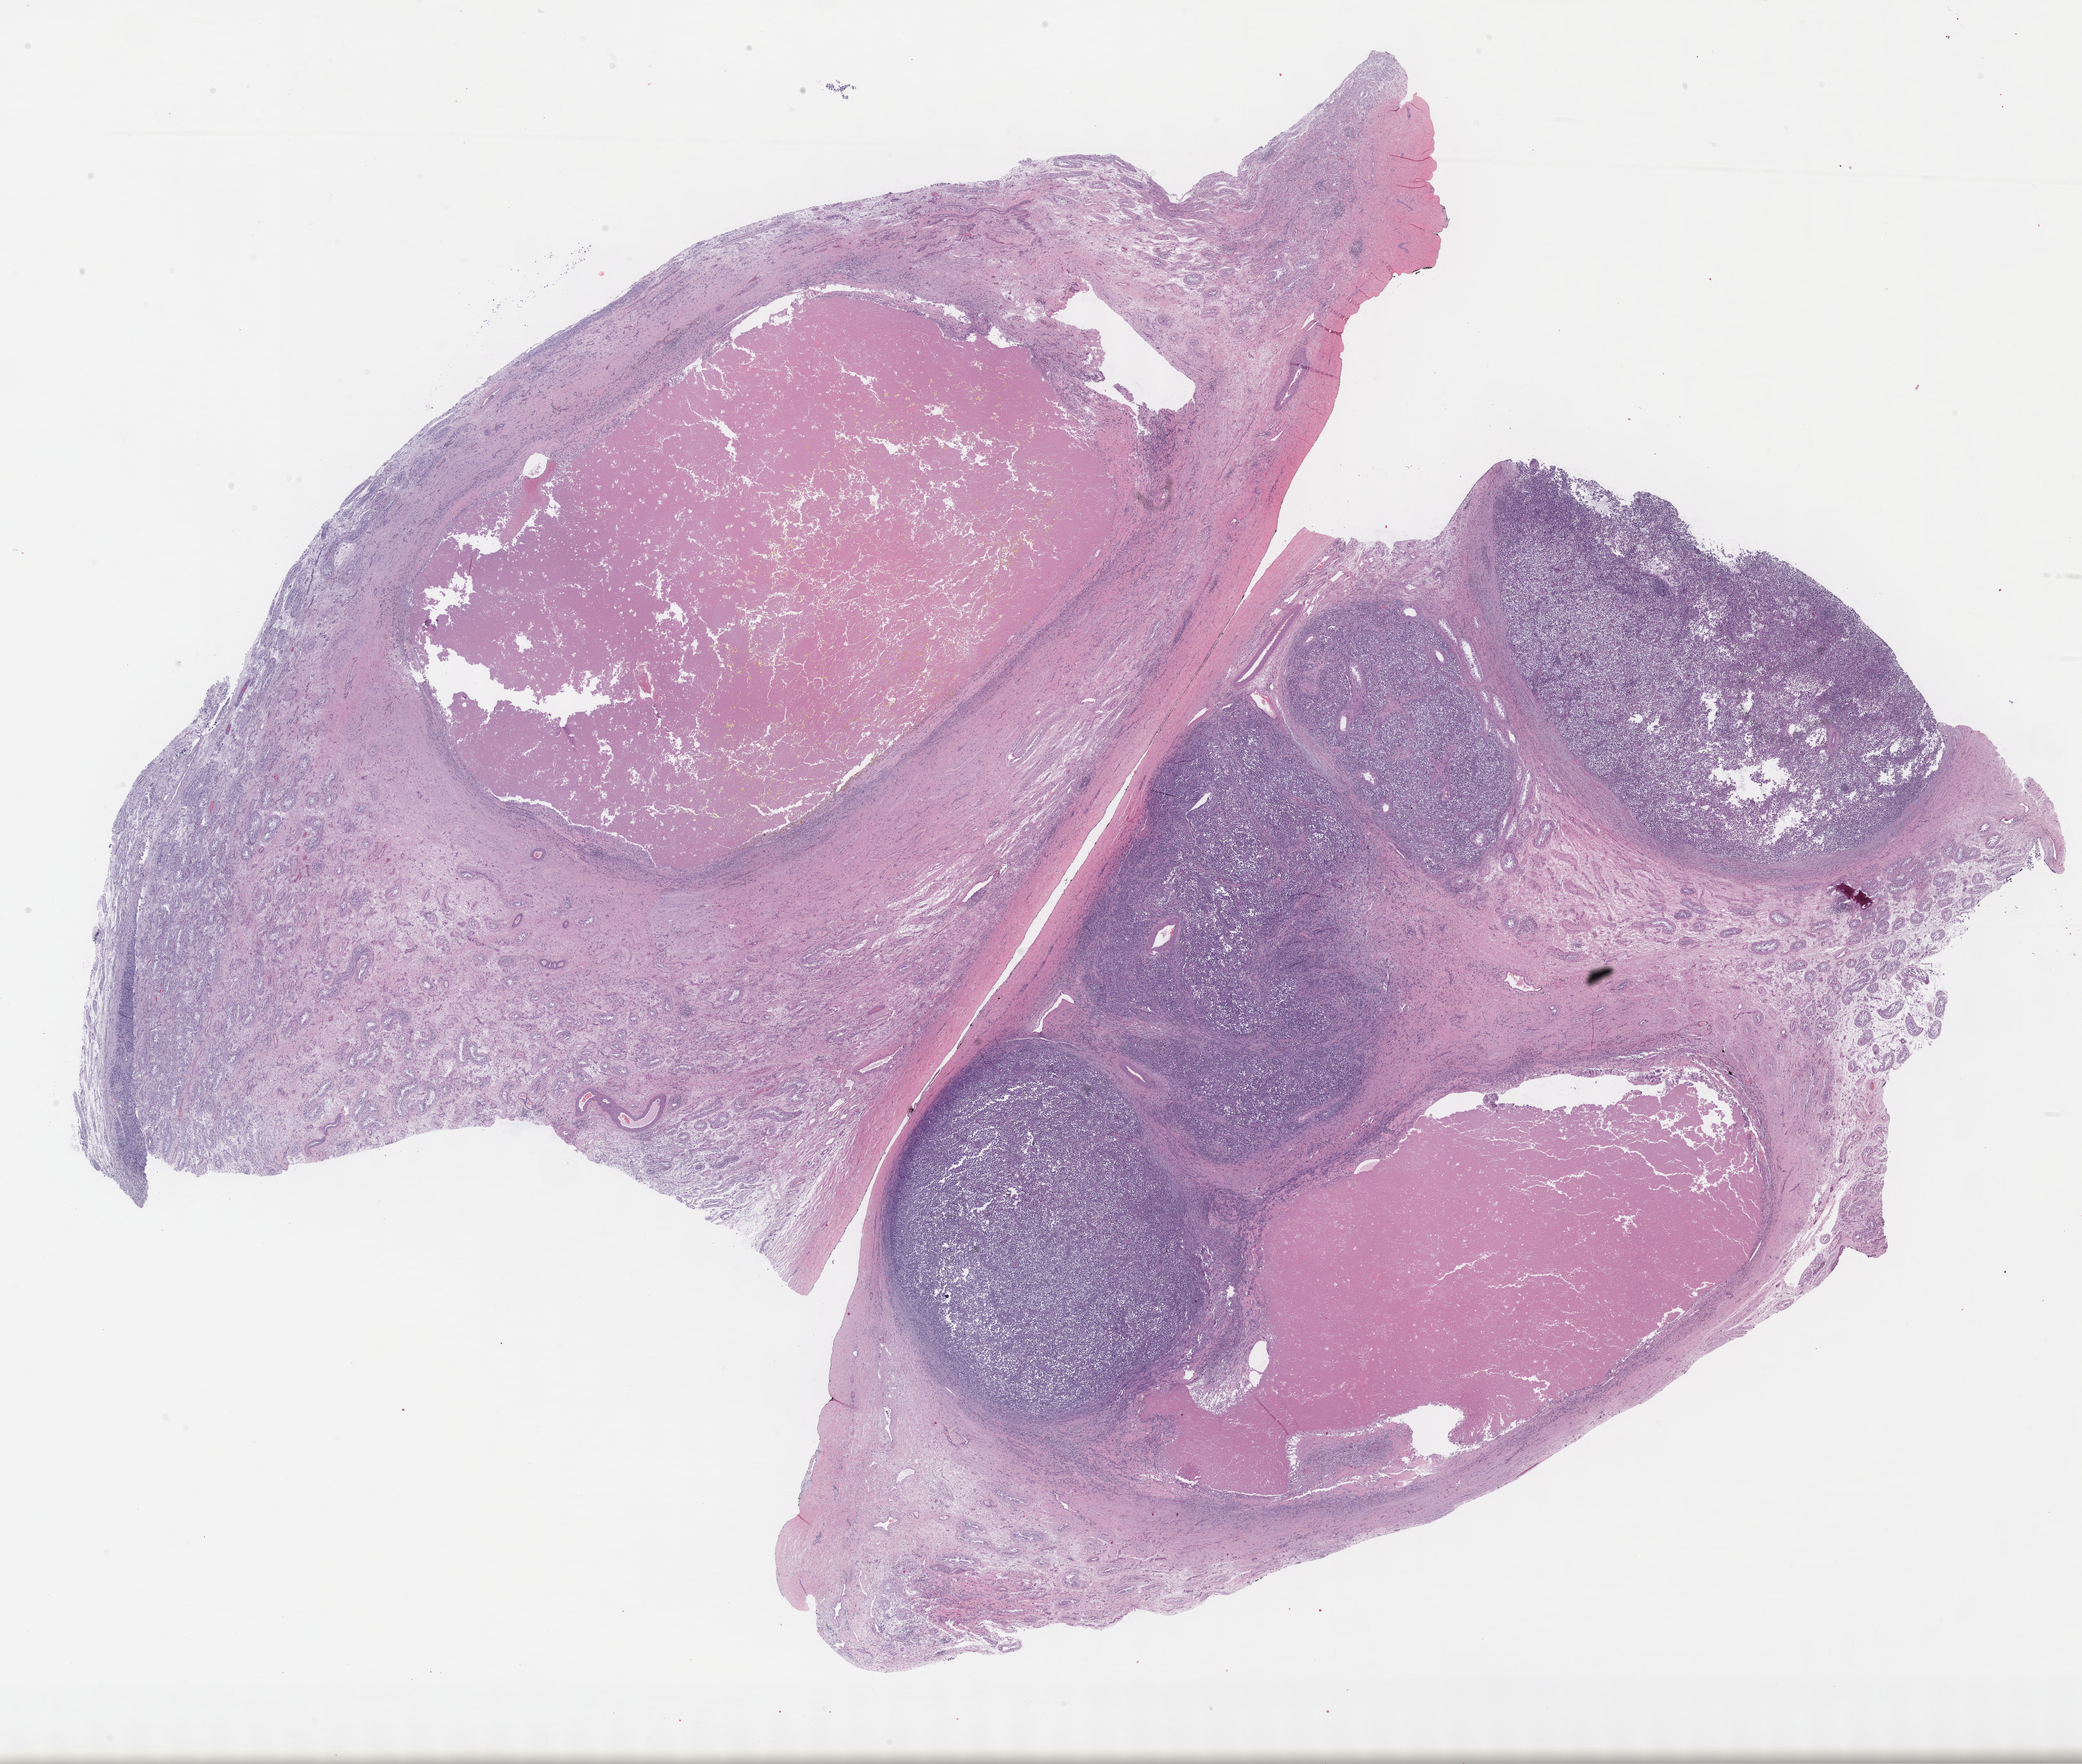
Whole-slide histology image, Hematoxylin and eosin (H&E) stained, whole scanned area (about 26.2 x 22.2 mm) shown as a low-resolution overview. FFPE section. Testis, primary tumour sample. Male, age 22 years at initial diagnosis.
* TNM: T1 NX M0
* AJCC pathologic stage: IA (7th edition)
* histologic diagnosis: Seminoma, NOS
* laterality: right